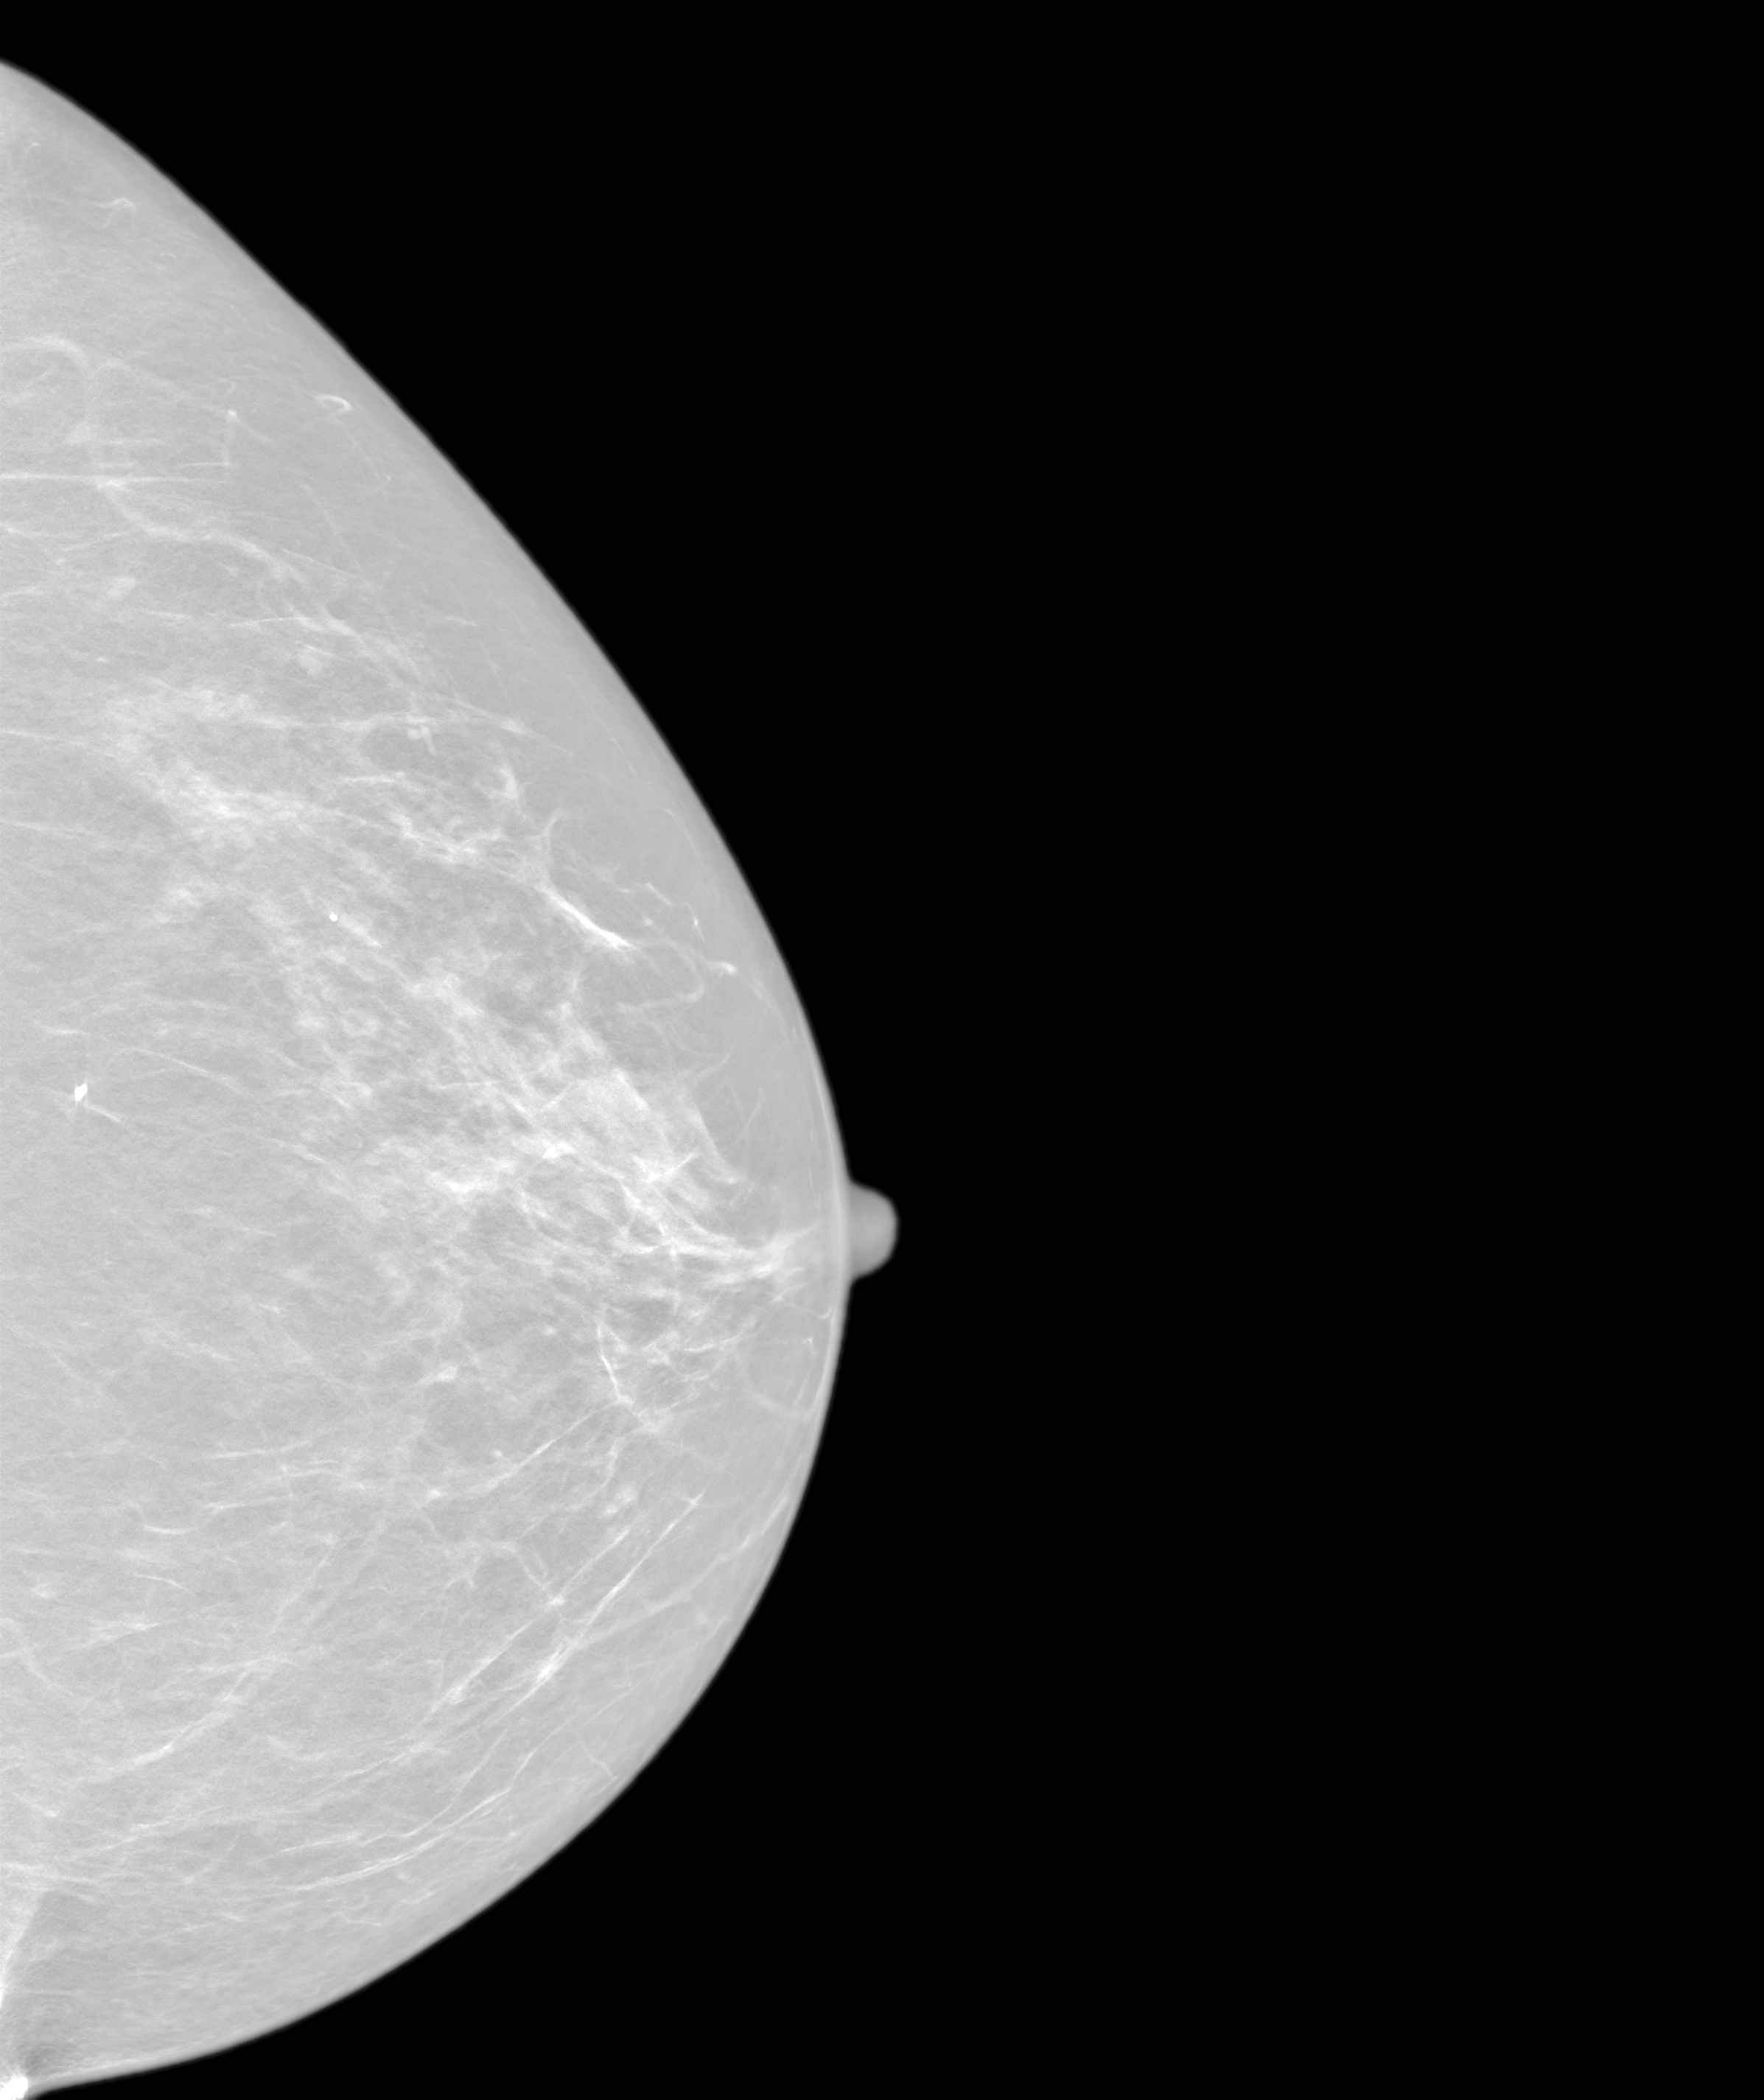
Screening examination. Patient: female, 54 years.
Image type: synthesized 2-D view from tomosynthesis. Breast: left. Projection: cranio-caudal projection.